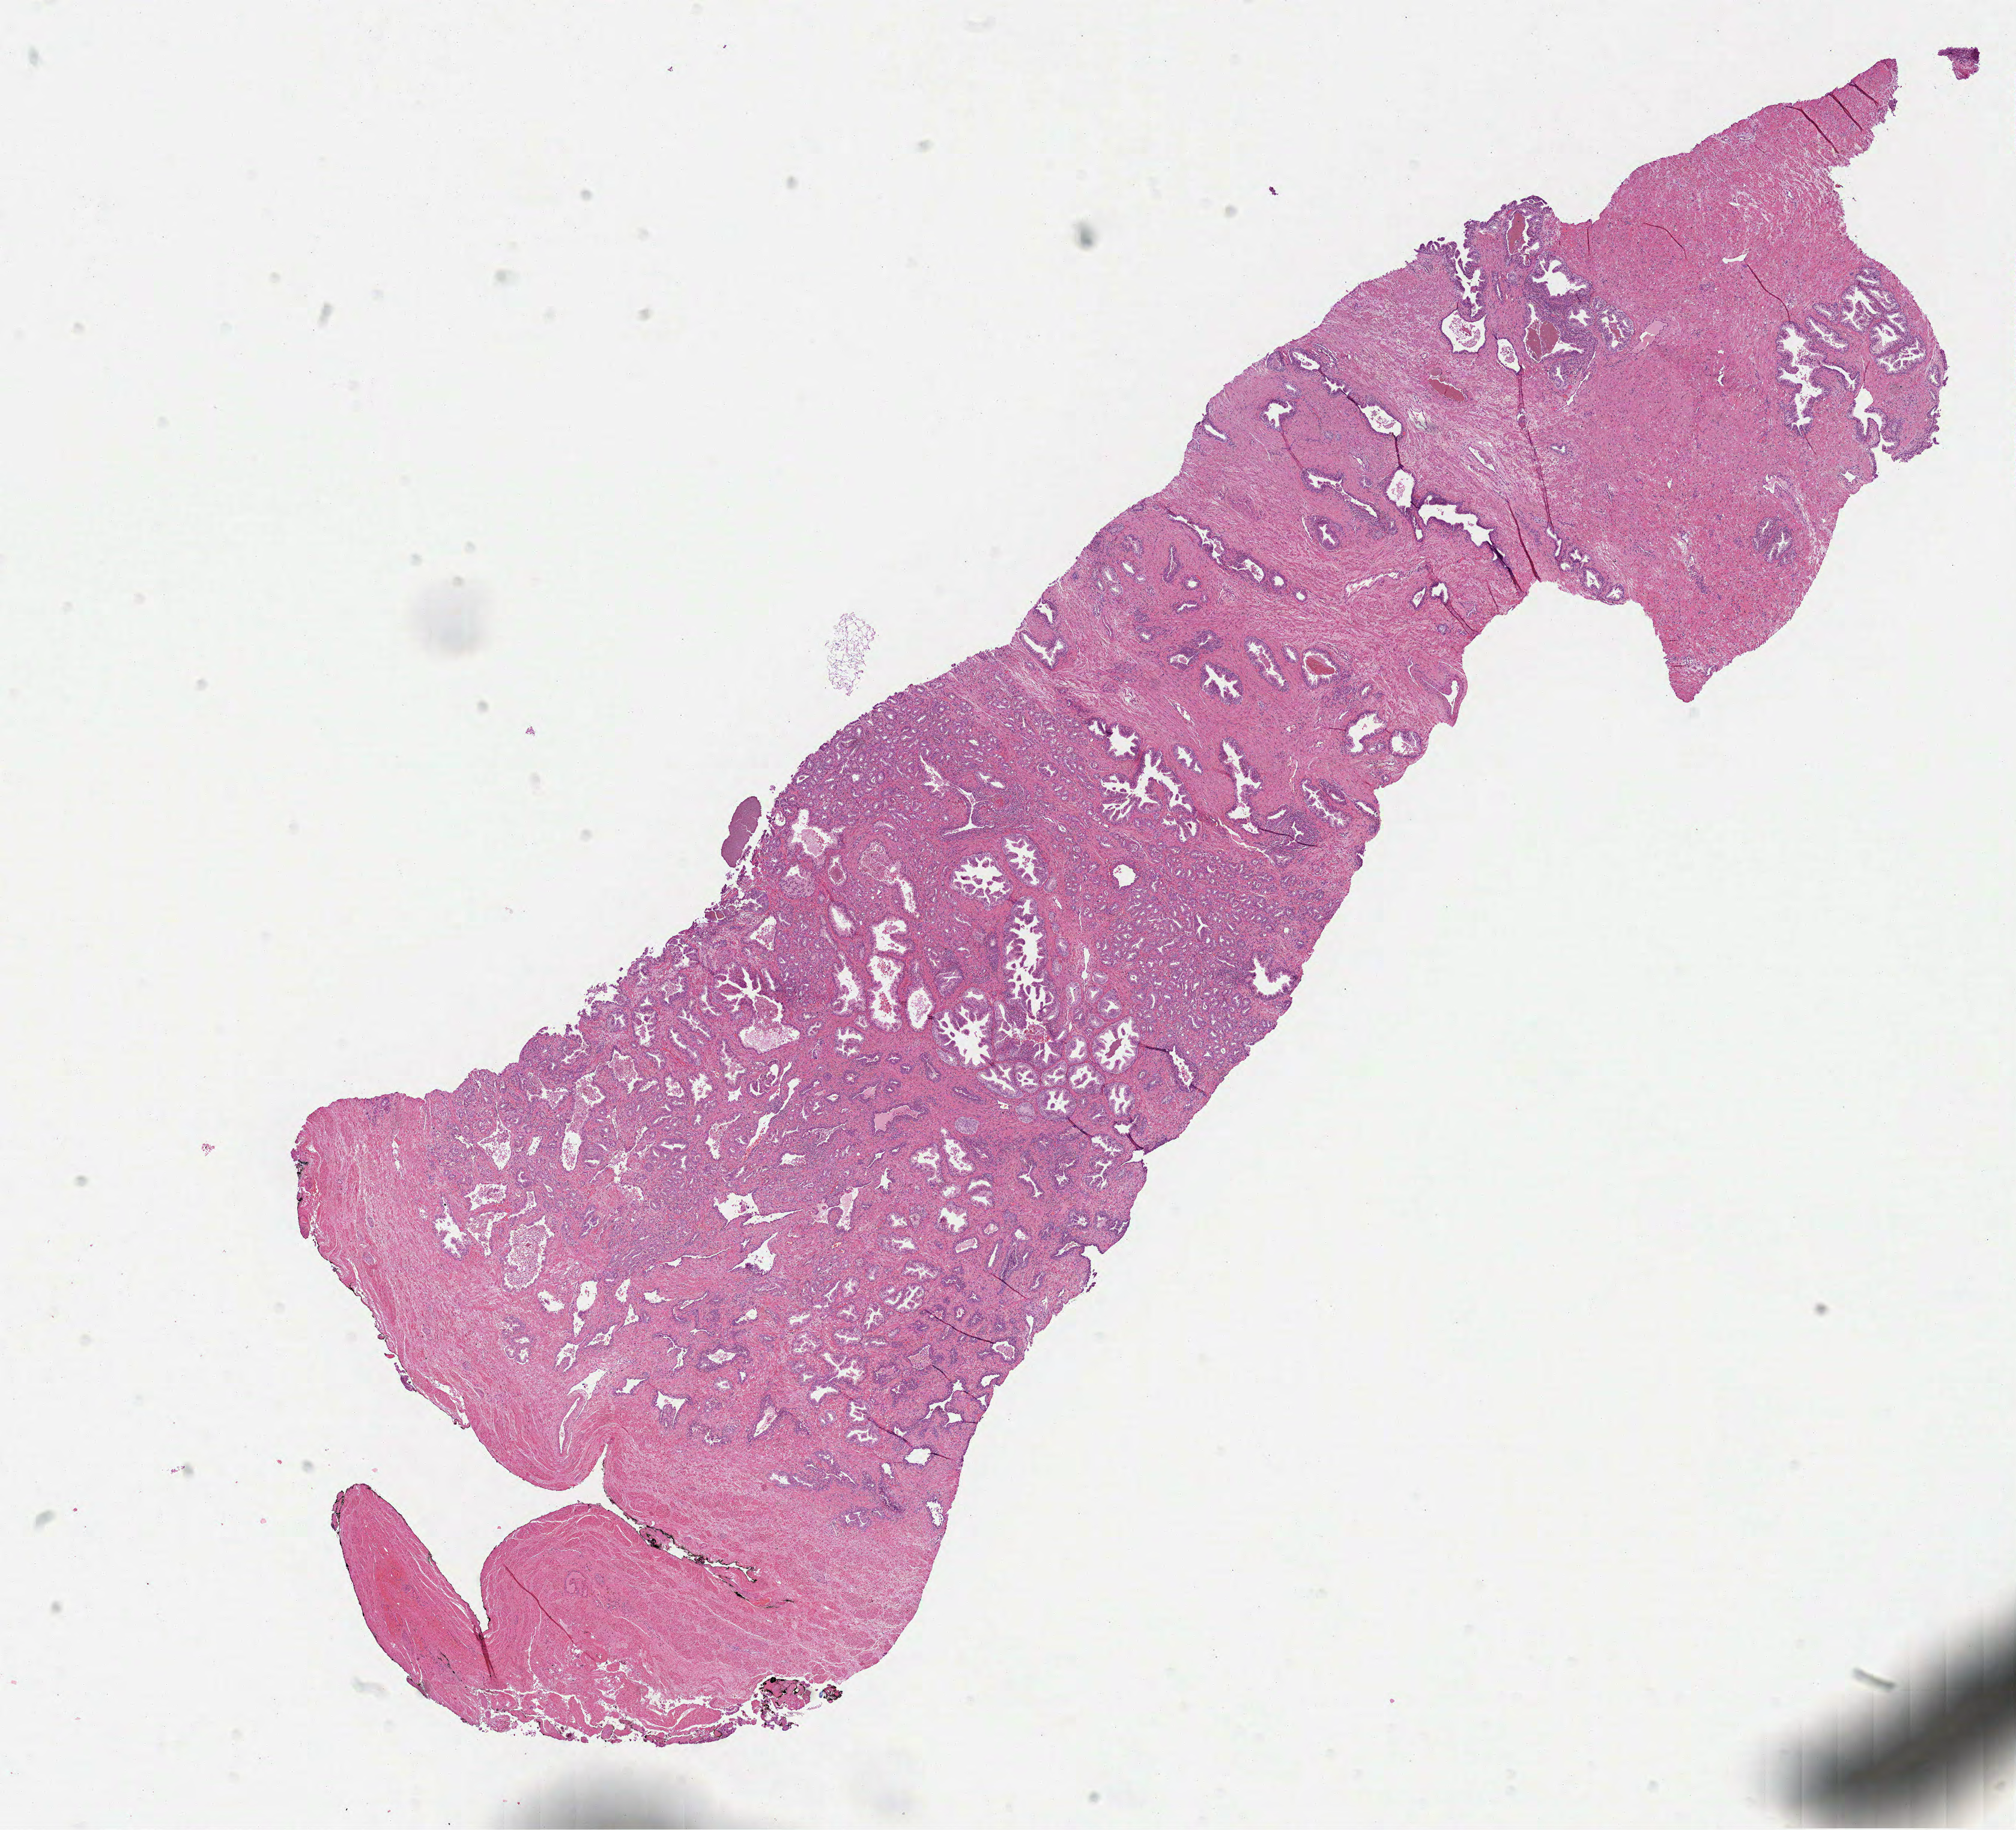
Whole-slide histology image, H&E-stained — a low-resolution overview of the entire scanned area, about 13.5 x 12.3 mm; formalin-fixed paraffin-embedded (FFPE) diagnostic section; sample: primary tumour, prostate. Male, age 56 years at initial diagnosis. Gleason score: 6 (3+3).
Pathologic diagnosis: Acinar cell carcinoma (prostate gland).